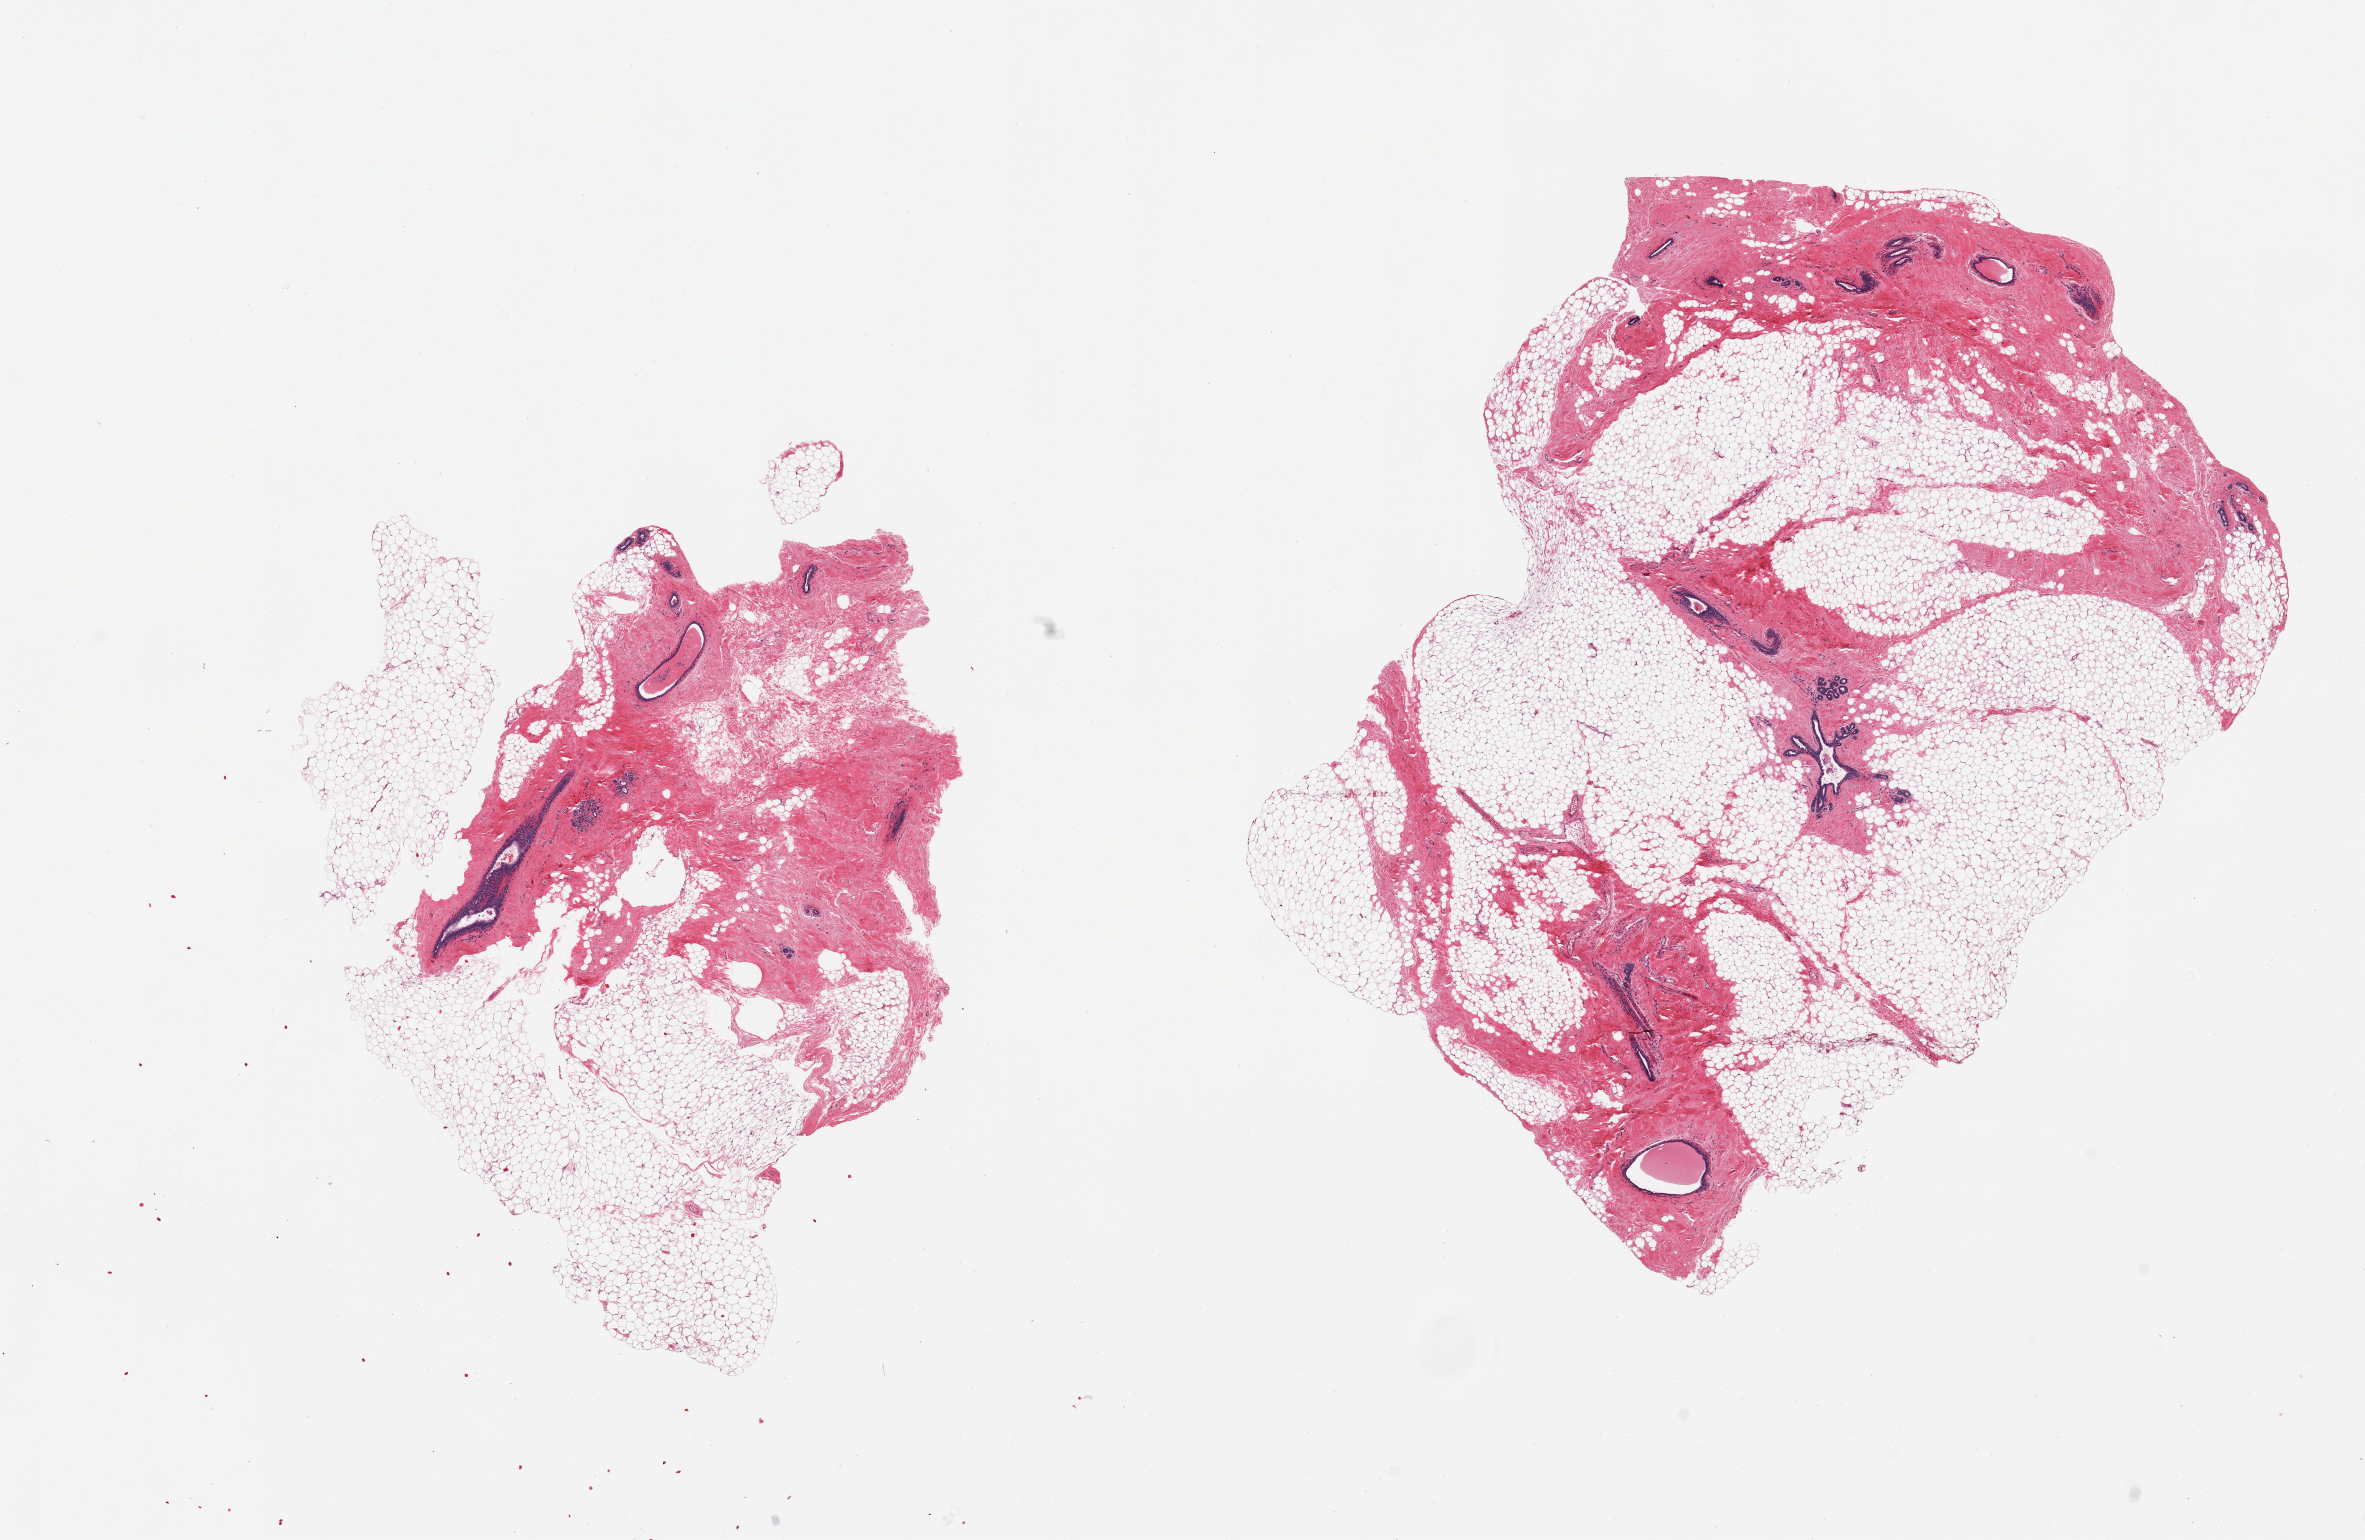
Hematoxylin and eosin (H&E) whole-slide image, a low-resolution overview of the entire scanned area, about 18.7 x 12.2 mm. PAXgene-fixed, paraffin-embedded tissue. Section of breast (target tissue). Tissue donor sample. Donor sex: female.
Review note (as recorded): 2 pieces; ductal-lobular units present; 50% adipose content.